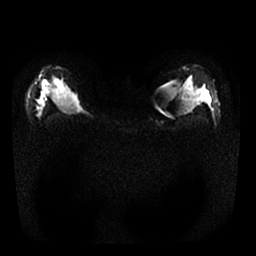
Breast MRI, one axial slice; position 16 of 25 along the scan axis; diffusion-weighted series; image 2 of 4 stored at this slice position (different b-values; order by instance number); 1.5 T; 256 × 256 image matrix, field of view 320 × 320 mm. Female patient.
Outlined on this slice (expert manual segmentation):
- tumour on diffusion-weighted imaging: bounding box [x1, y1, x2, y2] px = [42, 81, 47, 91]